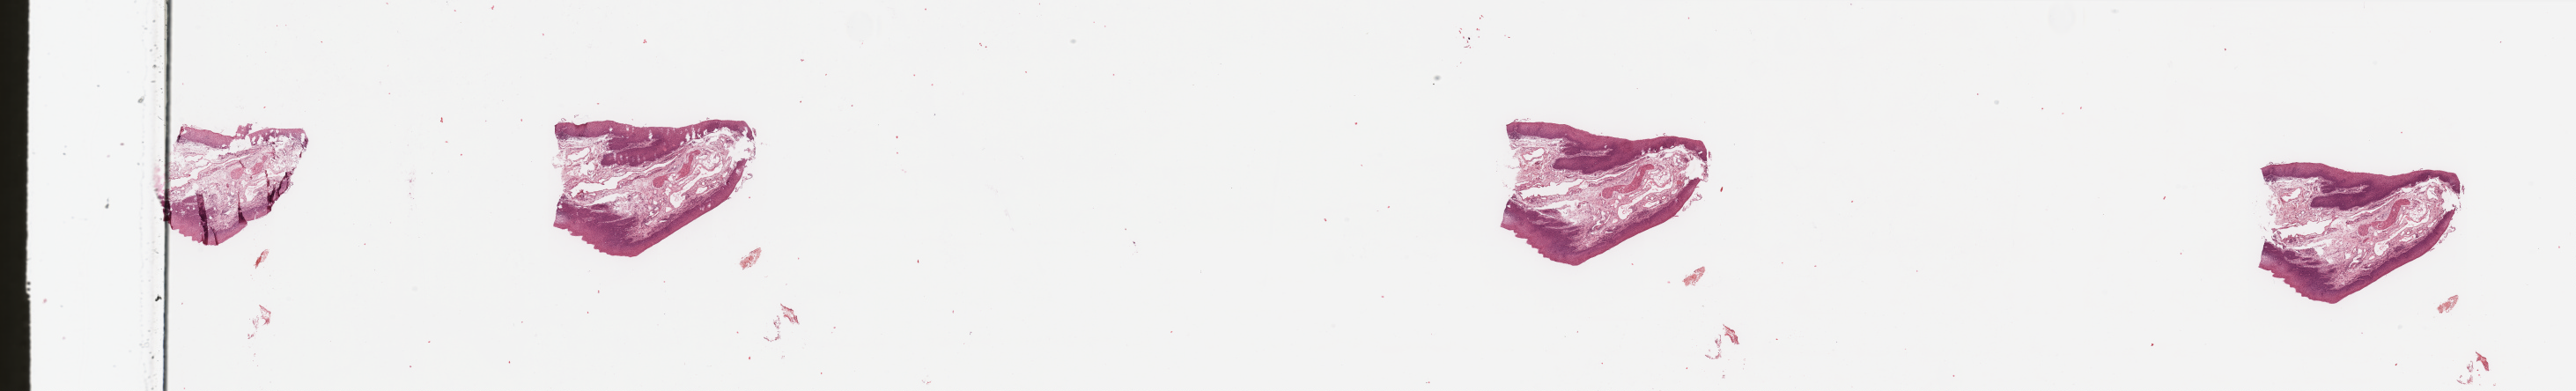
H&E whole-slide image — low-resolution overview of the scanned area, about 46.3 x 7.0 mm. Head and neck, normal (non-tumour) tissue. 61-year-old male patient.
- this section: normal (non-tumour) tissue from the same patient
- patient diagnosis: Squamous cell carcinoma, NOS (larynx, NOS)